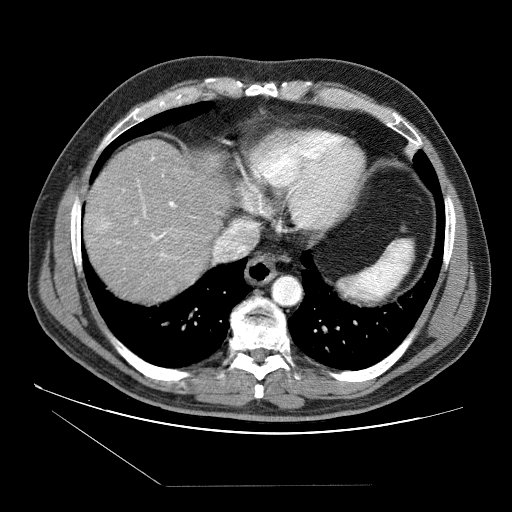
Contrast-enhanced abdominal CT (liver protocol), one axial slice. Position 73 of 87 along the scan axis. Reconstruction kernel STANDARD. Soft-tissue window (W 400 / L 40 HU). 512 × 512 image matrix, field of view 400 × 400 mm. Case-level facts recorded for this patient, not image findings: diagnosis: hepatocellular carcinoma (patient treated with transarterial chemoembolisation; whether this scan precedes or follows treatment is not stated here); TNM stage (as recorded): Stage-II; Child-Pugh class: B; tumour differentiation: no biopsy; tumour nodularity: multinodular.
Structures marked on this image (semi-automatic segmentation, software-assisted and operator-edited):
- abdominal aorta: box from (x=273, y=276) to (x=301, y=304) px
- liver parenchyma outside the tumour (the mass and vessels are separate outlines, so this box may not span the whole liver): (x=84, y=140)–(x=232, y=300)
- liver vessels: (x=97, y=157)–(x=178, y=259)